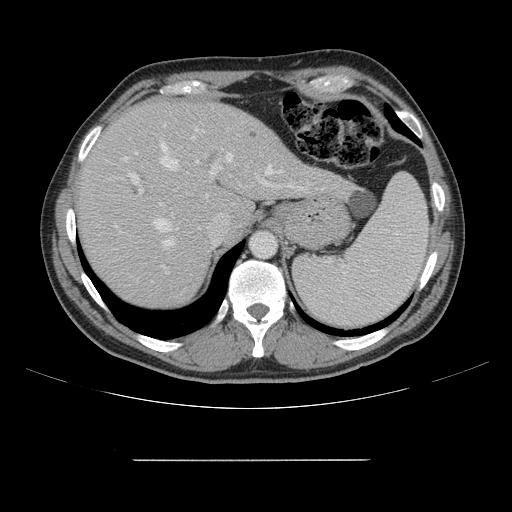
Contrast-enhanced abdominal CT, one axial slice. Slice 117 of 164 in the series (ordered by position). 120 kVp. Intravenous contrast given. Soft-tissue window (W 400 / L 40 HU). 2.5 mm slice thickness. 512 × 512 image matrix, field of view 404 × 404 mm. Male patient, age 54 years. Case-level facts recorded for this patient, not image findings: diagnosis: colorectal cancer liver metastases, imaged before liver resection.
Annotated regions visible in this slice (outlined manually by an expert reader):
- hepatic veins: bounding box <152,143,283,282> (left, top, right, bottom; pixels)
- liver: <78,103,345,305>
- planned liver remnant (the part of the liver to remain after resection): <78,103,249,306>
- portal vein (with intrahepatic branches): <116,125,303,282>